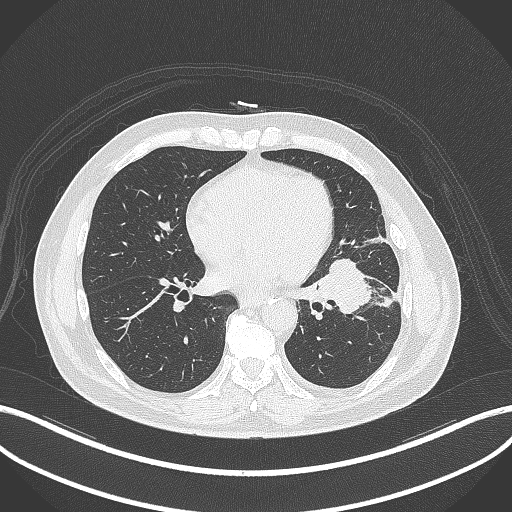
Chest CT, one axial slice; position 151 of 230 along the scan axis; 120 kVp; lung window (W 1500 / L -600 HU); 1 mm slice thickness; 512 × 512 image matrix. Patient: male, 68 years. Case-level facts recorded for this patient, not image findings: clinical TNM (as recorded): T2b N0 M0.
Outlined on this slice (bounding box drawn by a radiologist):
- lung tumour (recorded histology: squamous cell carcinoma): bounding box <311,253,378,318> (left, top, right, bottom; pixels)